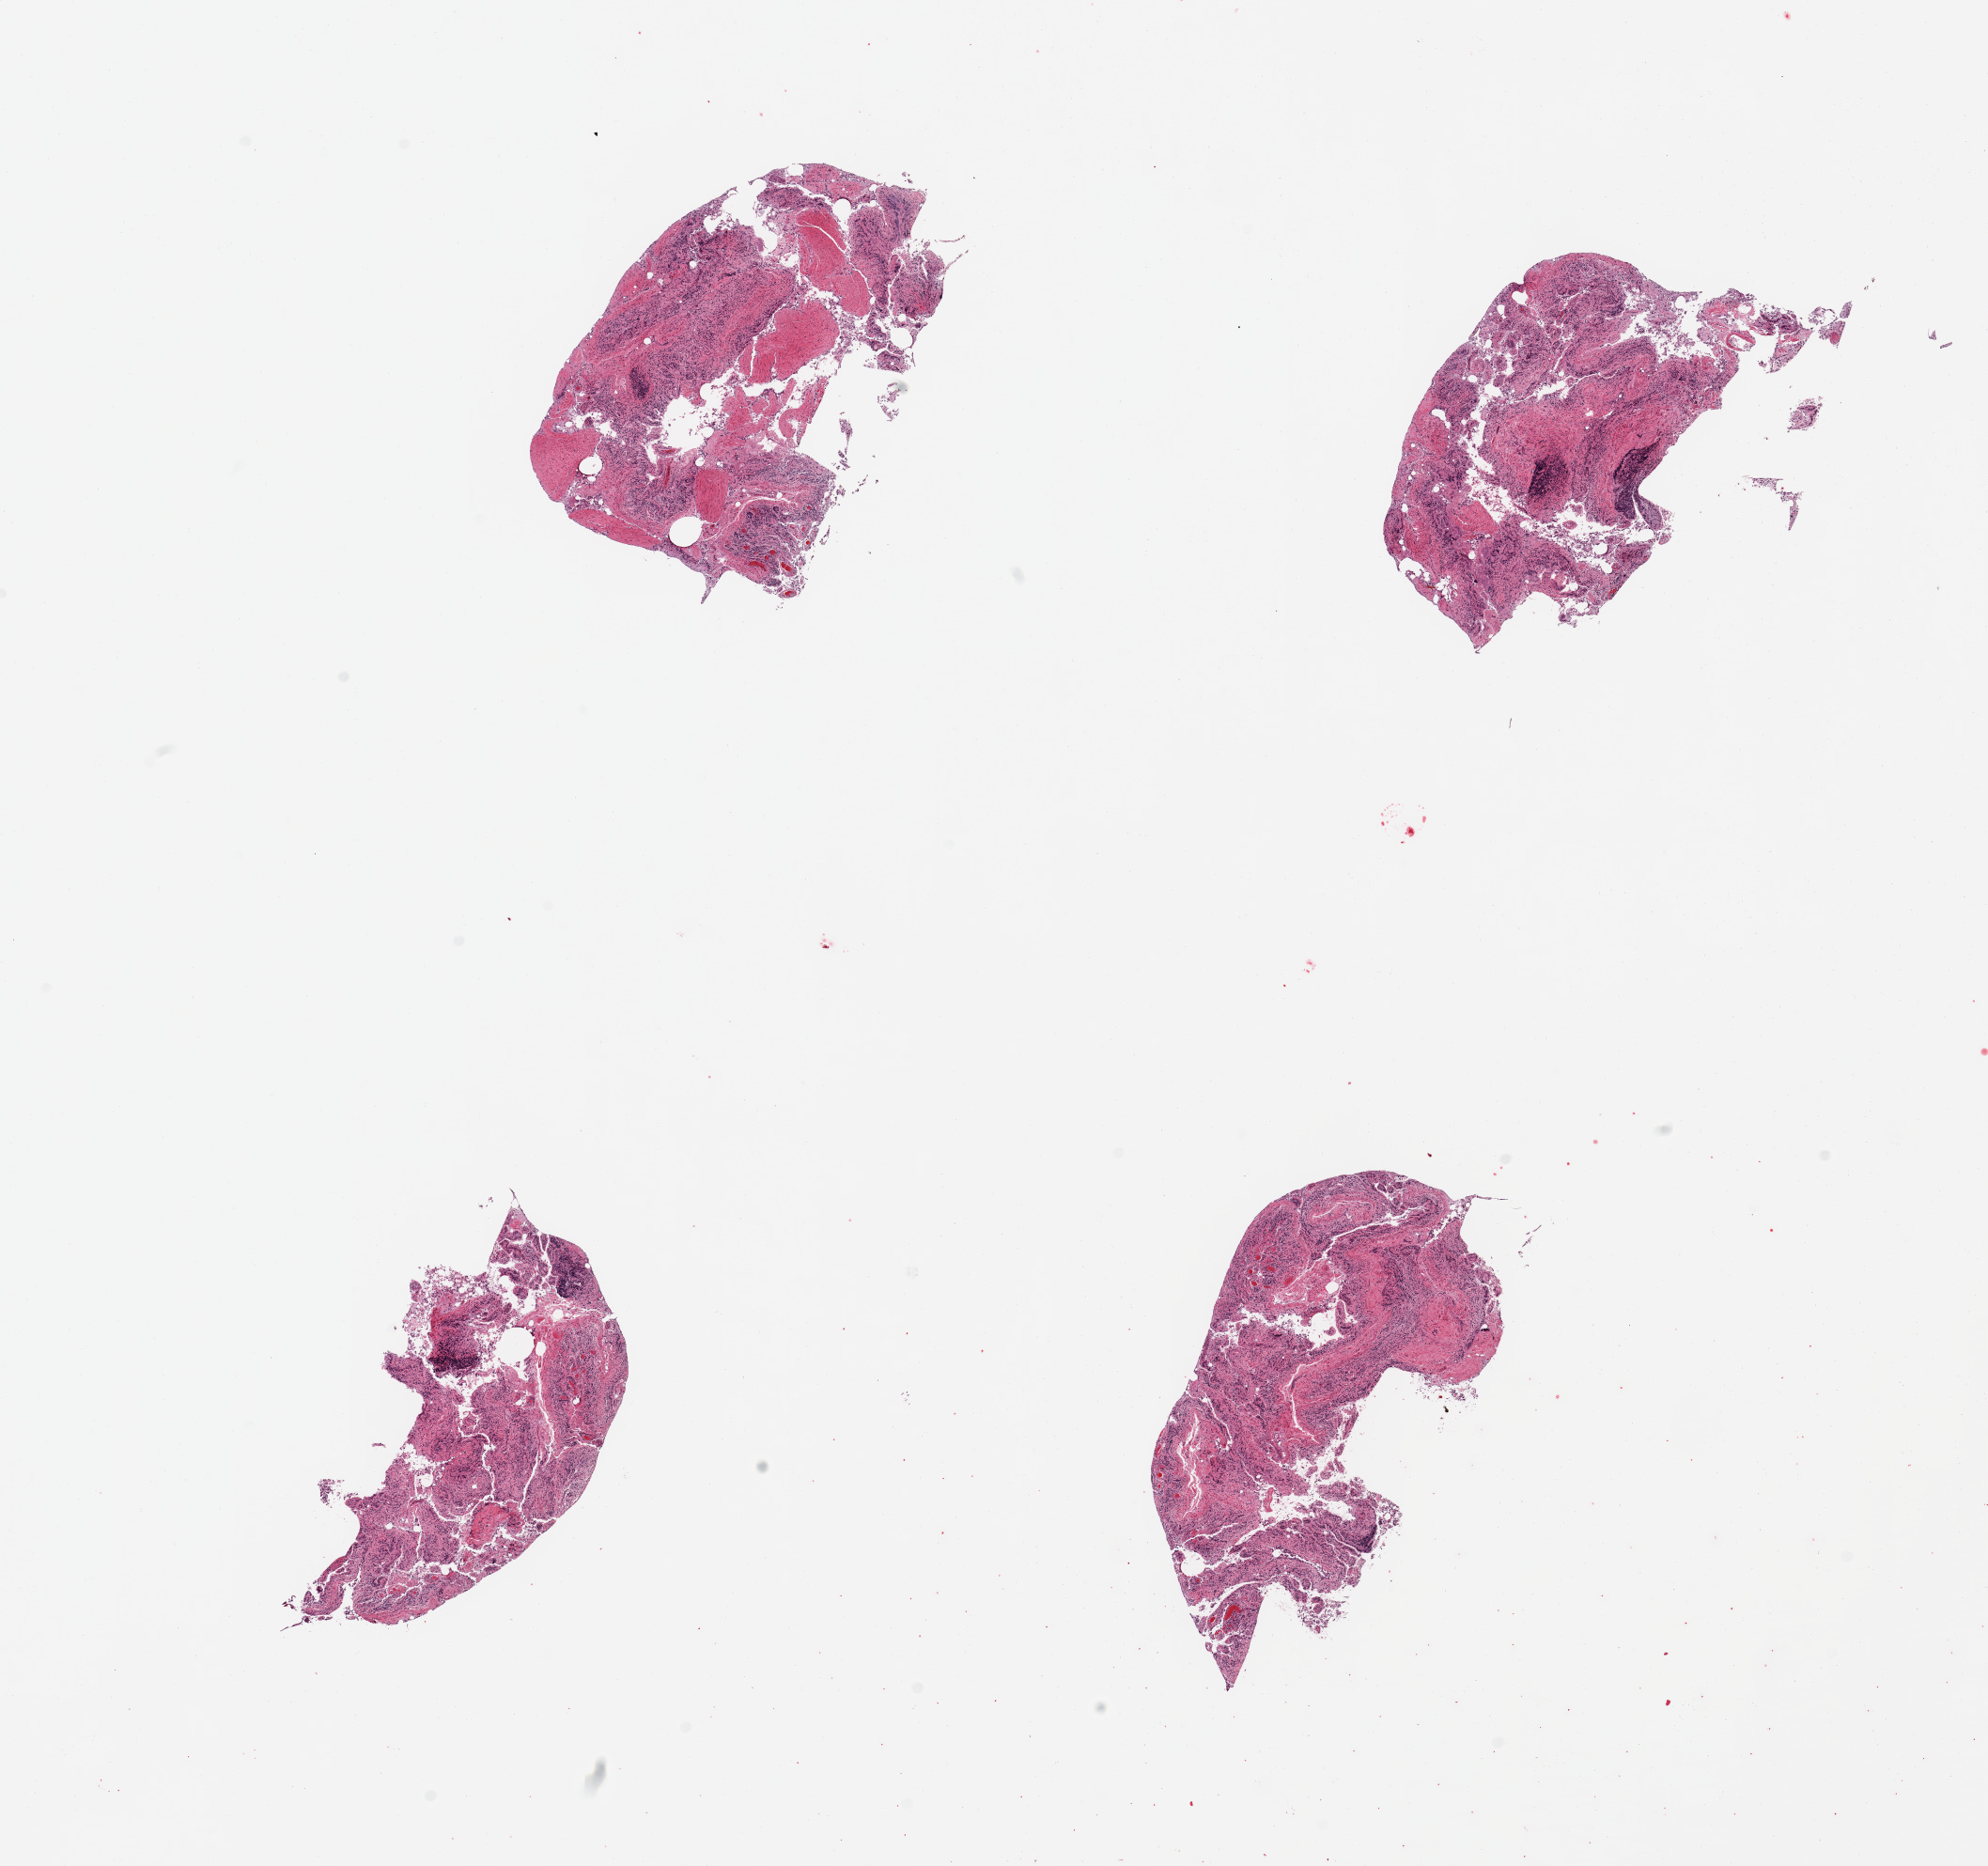
Digitized hematoxylin and eosin (H&E)-stained section, brightfield — whole scanned area (about 16.7 x 15.7 mm) shown as a low-resolution overview, PAXgene-fixed, paraffin-embedded tissue, sampled site (target tissue): ileum, donor tissue sample. Male donor.
Reviewer comment on this tissue sample: 4 pieces; too little lymphoid tissue.